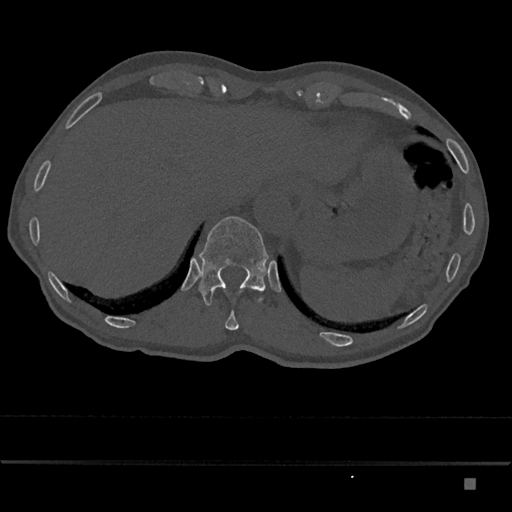
CT including the spine, one axial slice; position 634 of 797 along the scan axis; reconstruction kernel Br40s/3; 120 kVp; bone window (W 1800 / L 400 HU); 0.5 mm slice thickness; 512 × 512 image matrix. Patient: male, 72 years. Case-level facts recorded for this patient, not image findings: primary cancer: prostate.
Structures marked on this image (semi-automatically segmented with operator editing):
- T11 vertebra: bounding box (x1, y1, x2, y2) in pixels: (225, 310, 239, 330)
- T12 vertebra: (198, 216, 269, 306)